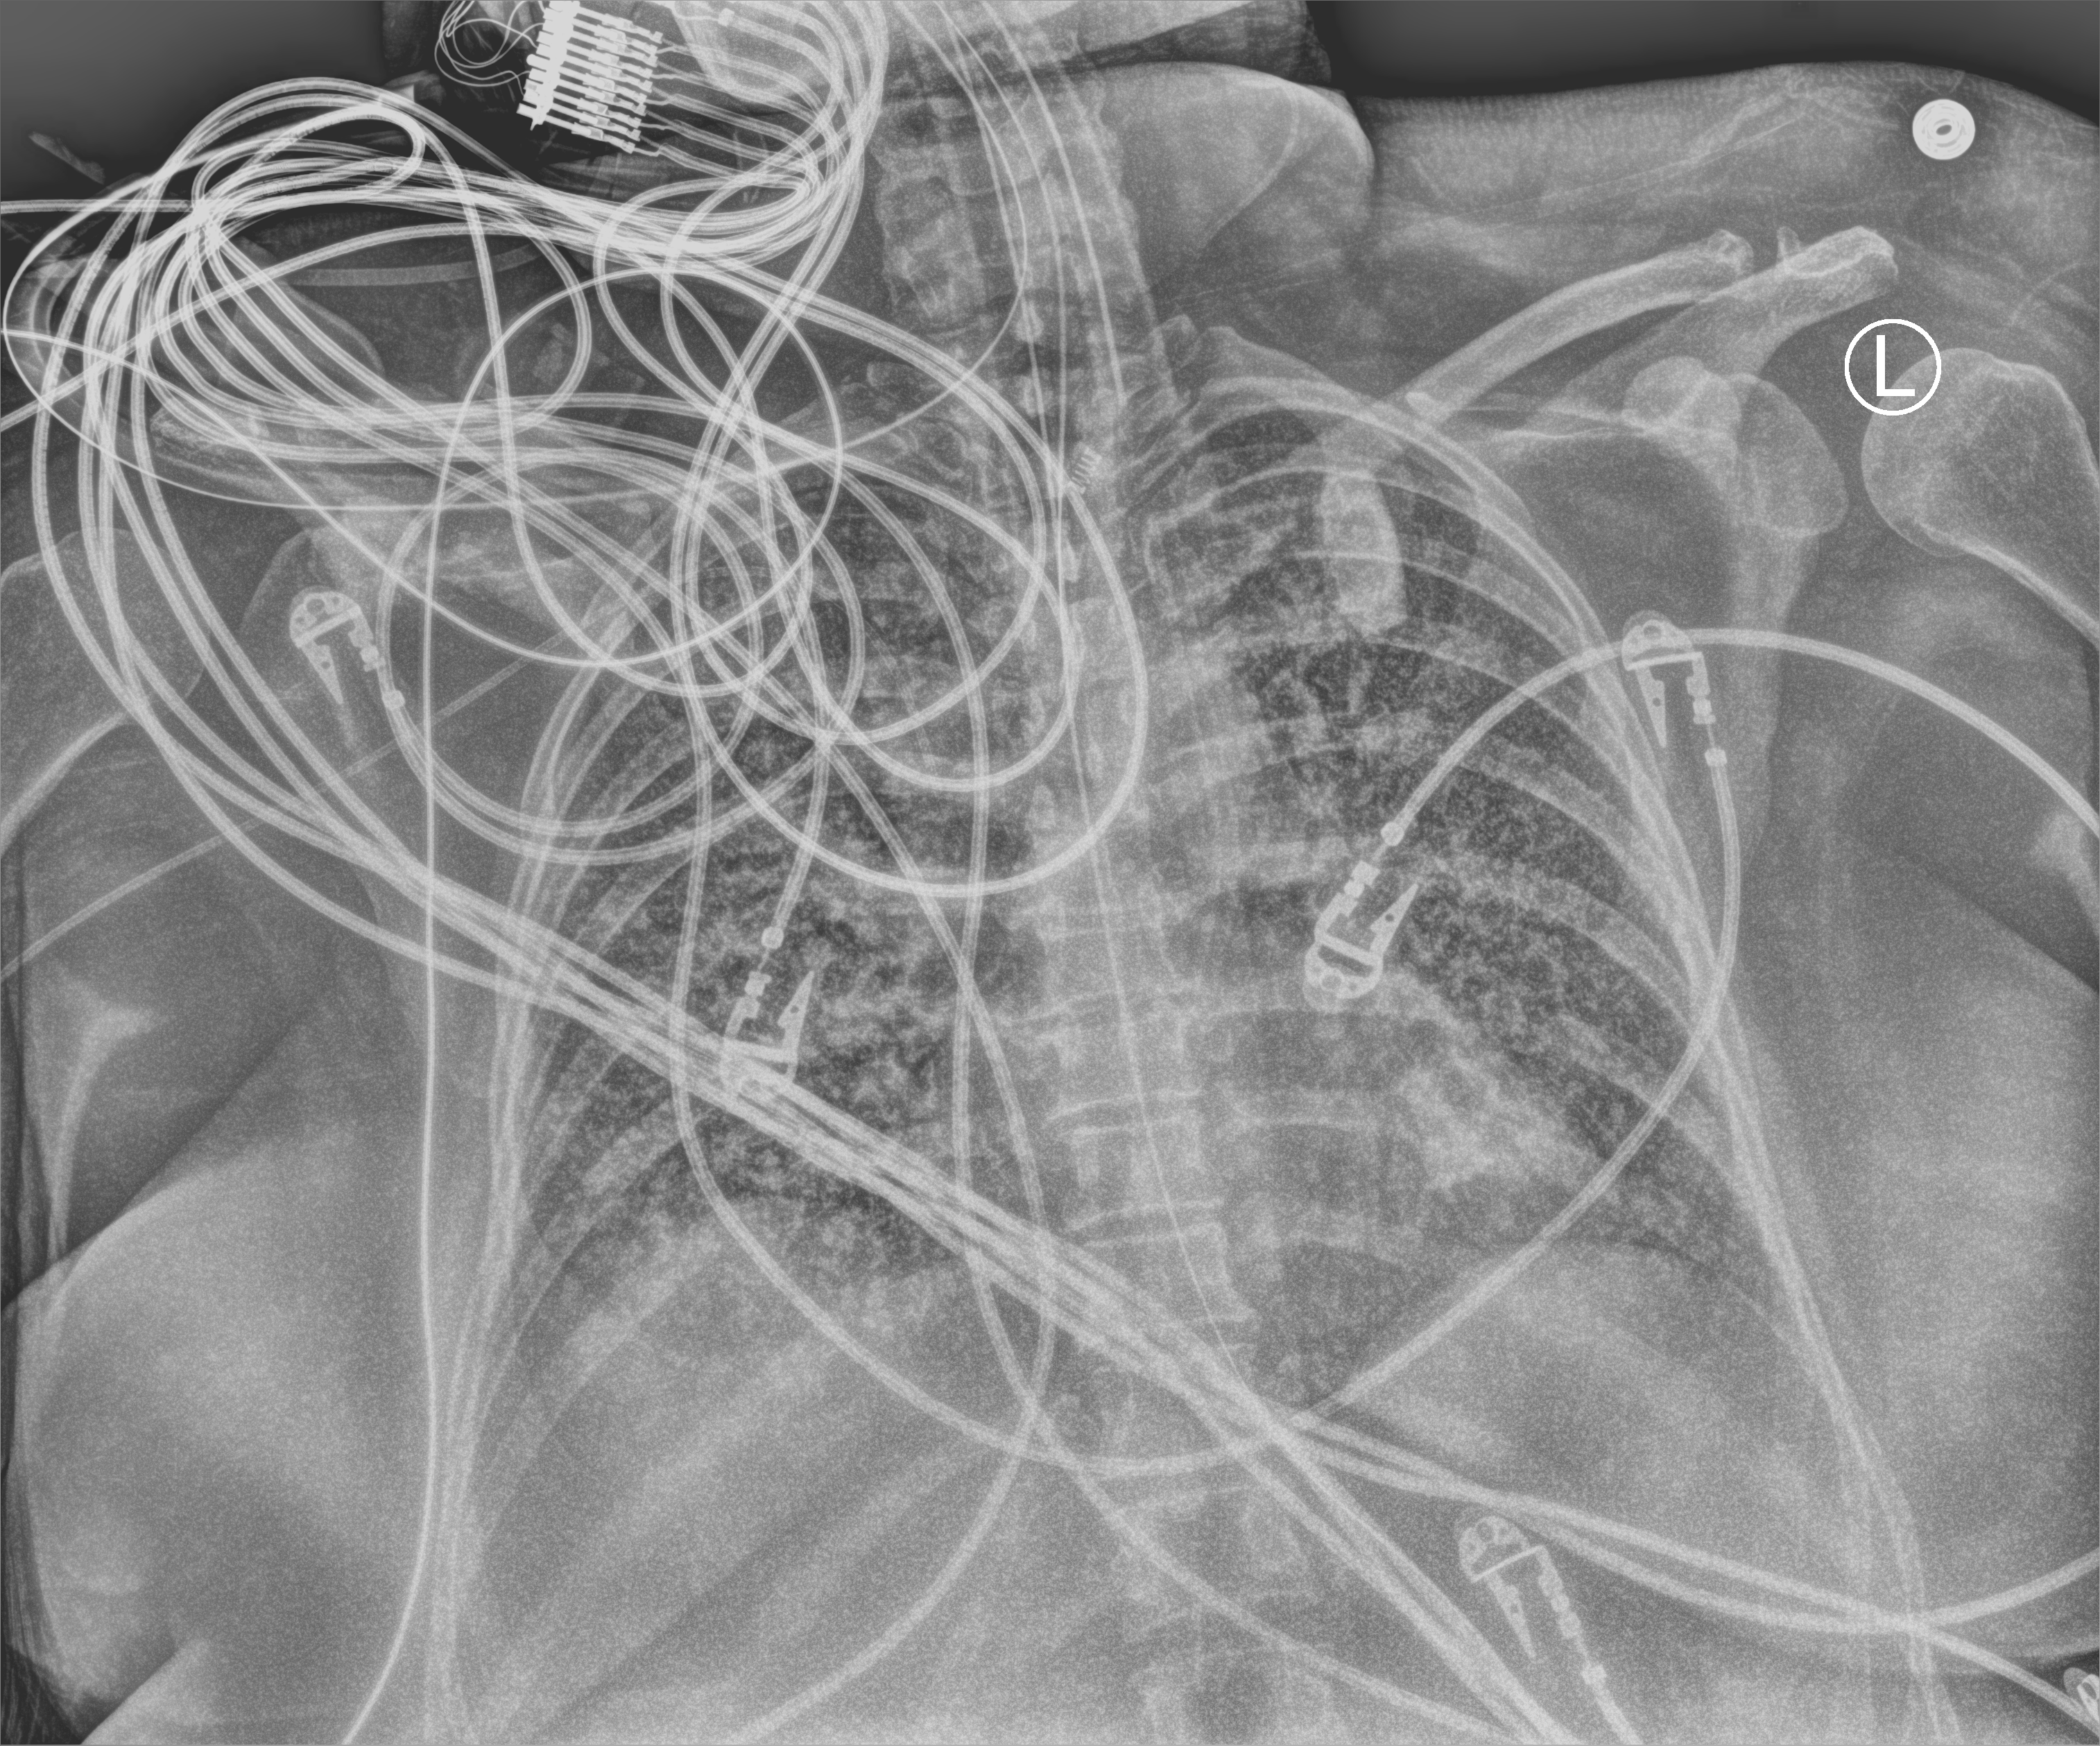
Chest X-ray (portable), anteroposterior (AP) projection. Female patient hospitalised with COVID-19, age 18–59 years.
From the hospital-stay record, not from the radiograph (when in the stay this image was taken is not recorded): admitted to intensive care during this hospital stay: yes; COPD (admission record): no; length of hospital stay: 95 days.